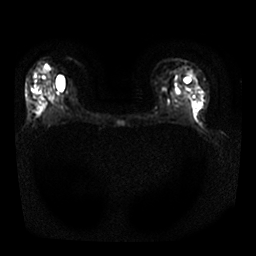
Breast MRI, one axial slice. Slice 17 of 25 in the series (ordered by position). Diffusion-weighted series; image 2 of 4 stored at this slice position (different b-values; order by instance number). 1.5 T. 4 mm slice thickness. 256 × 256 image matrix. Female patient.
Annotated regions visible in this slice (outlined manually by an expert reader):
- tumour on diffusion-weighted imaging: box from (x=35, y=69) to (x=48, y=113) px